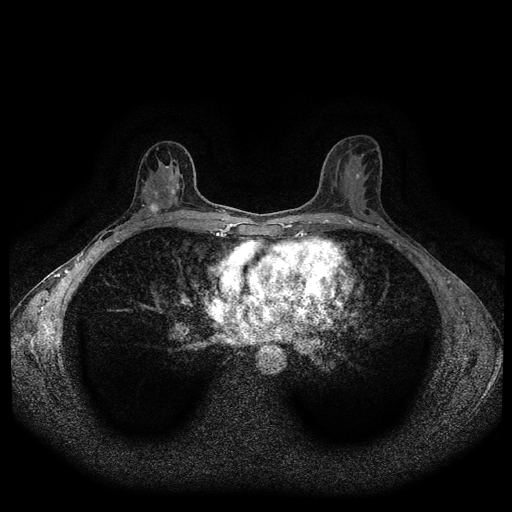
Breast MRI (dynamic contrast-enhanced, multi-phase), one axial slice; position 58 of 116 along the scan axis; dynamic contrast-enhanced series, time point 2 of 5 at this slice position (early post-contrast); 1.5 T; TE 2.6 ms, TR 5.3 ms; 2 mm slice thickness; 512 × 512 image matrix, field of view 350 × 350 mm. Female patient, age 50 years.
Annotated regions visible in this slice (semi-automatic segmentation, software-assisted and operator-edited):
- breast lesion (labelled 'tumour' in the annotation; benign lesions carry a separate 'benign' label): box from (x=147, y=198) to (x=160, y=215) px